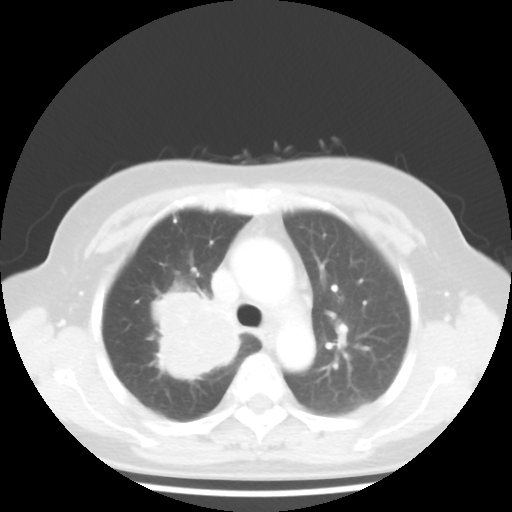
Chest CT, one axial slice; slice 31 of 44 in the series (ordered by position); lung window (W 1500 / L -600 HU); 5 mm slice thickness; 512 × 512 image matrix, field of view 316 × 316 mm. Patient: female, 62 years. From the clinical record (not read from this slice): clinical TNM (as recorded): T3 N0 M0; histopathological grade: G3.
Outlined on this slice (rectangle marked by the reading radiologist):
- lung tumour (recorded histology: small cell carcinoma): bounding box [x1, y1, x2, y2] px = [145, 283, 245, 381]